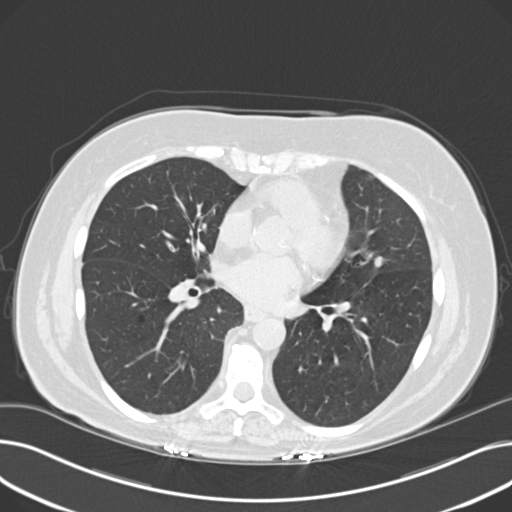
Low-dose screening chest CT, one axial slice. Reconstruction kernel B30f. Lung window (W 1500 / L -600 HU). 2 mm slice thickness. 512 × 512 image matrix.
Outlined on this slice (manually delineated by an expert):
- lesion 1 (tumor, upper lobe of left lung): bounding box <374,256,385,268> (left, top, right, bottom; pixels)